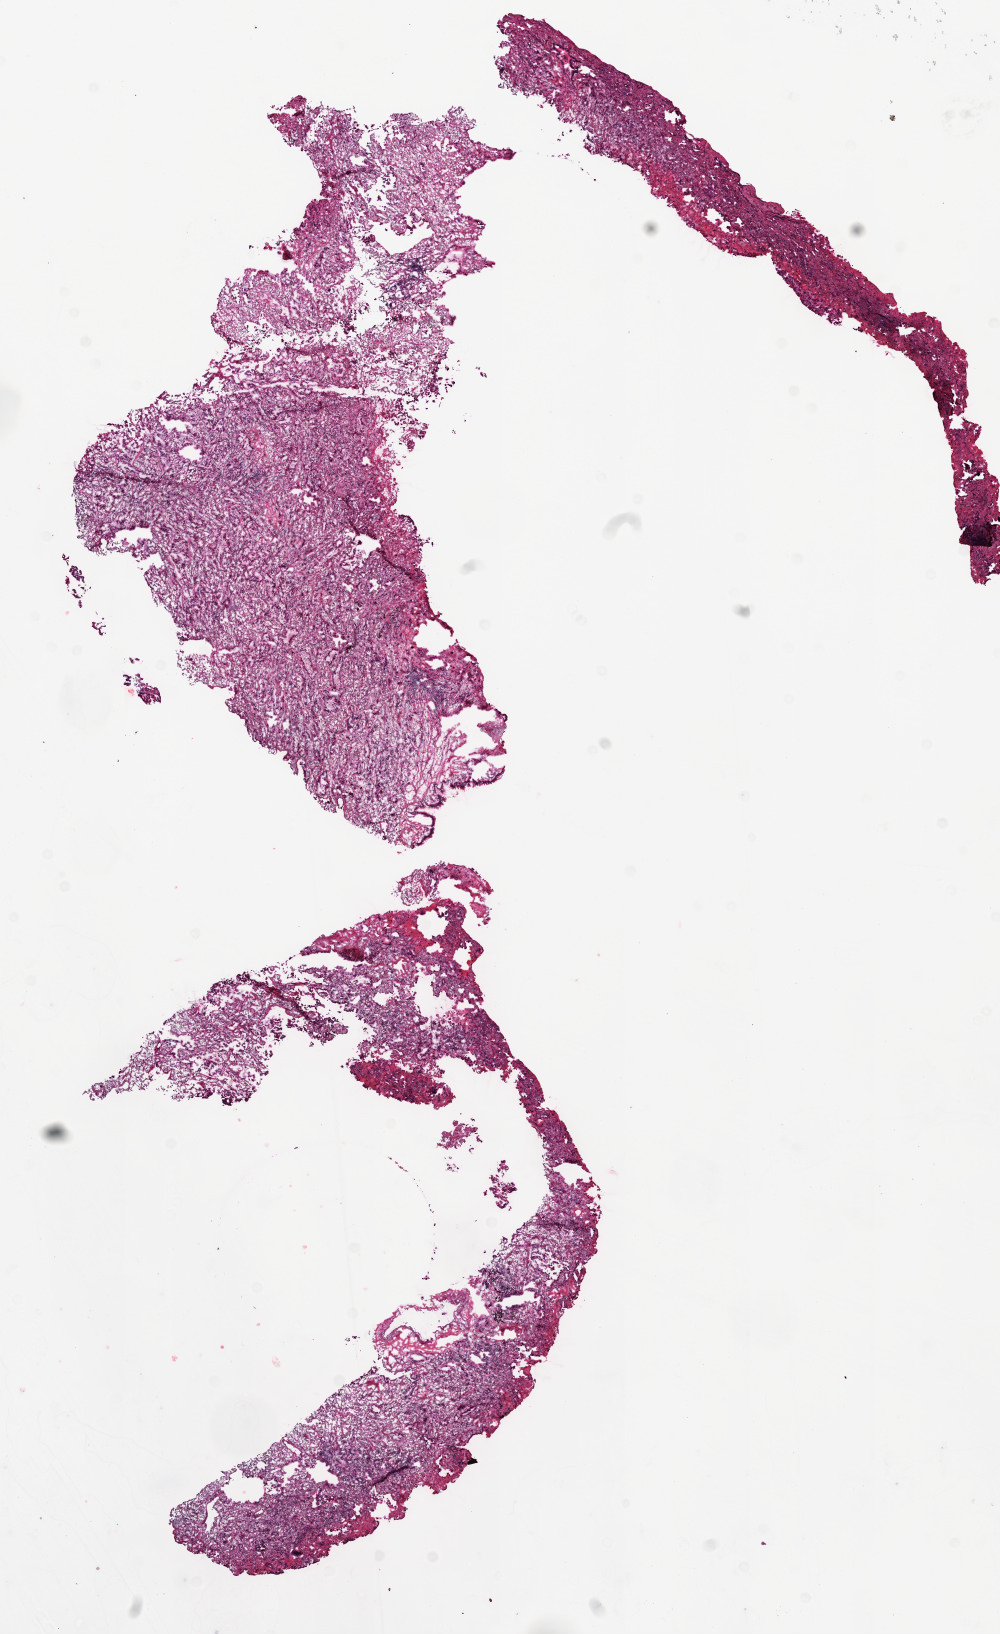
Digitized H&E tissue section (whole slide), a low-resolution overview of the entire scanned area, about 8.0 x 13.1 mm (slide scanned at 20x). Frozen section from the top of the tissue portion. Lung, primary tumour sample. Female patient; age at initial diagnosis 61 years. Pathologist review of this section (percent, as recorded): tumour cells 5%, tumour nuclei 15%, normal cells 0%, stromal cells 5%, necrosis 90%. Infiltration values recorded for this section: lymphocyte infiltration 85%, monocyte infiltration 9%, neutrophil infiltration 5%.
* pathologic diagnosis: Adenocarcinoma, NOS
* TNM: T1 N0 M0
* AJCC pathologic stage: IA (6th edition)